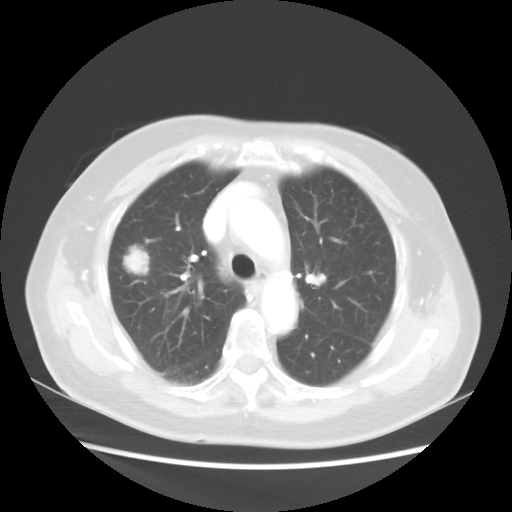
Chest CT, one axial slice; slice 33 of 48 in the series (ordered by position); reconstruction kernel STANDARD; lung window (W 1500 / L -600 HU); 5 mm slice thickness; 512 × 512 image matrix. Patient: female, 75 years. Case-level facts recorded for this patient, not image findings: clinical TNM (as recorded): T1c N0 M0.
Structures marked on this image (bounding box drawn by a radiologist):
- lung tumour (recorded histology: adenocarcinoma): bounding box <122,246,151,280> (left, top, right, bottom; pixels)